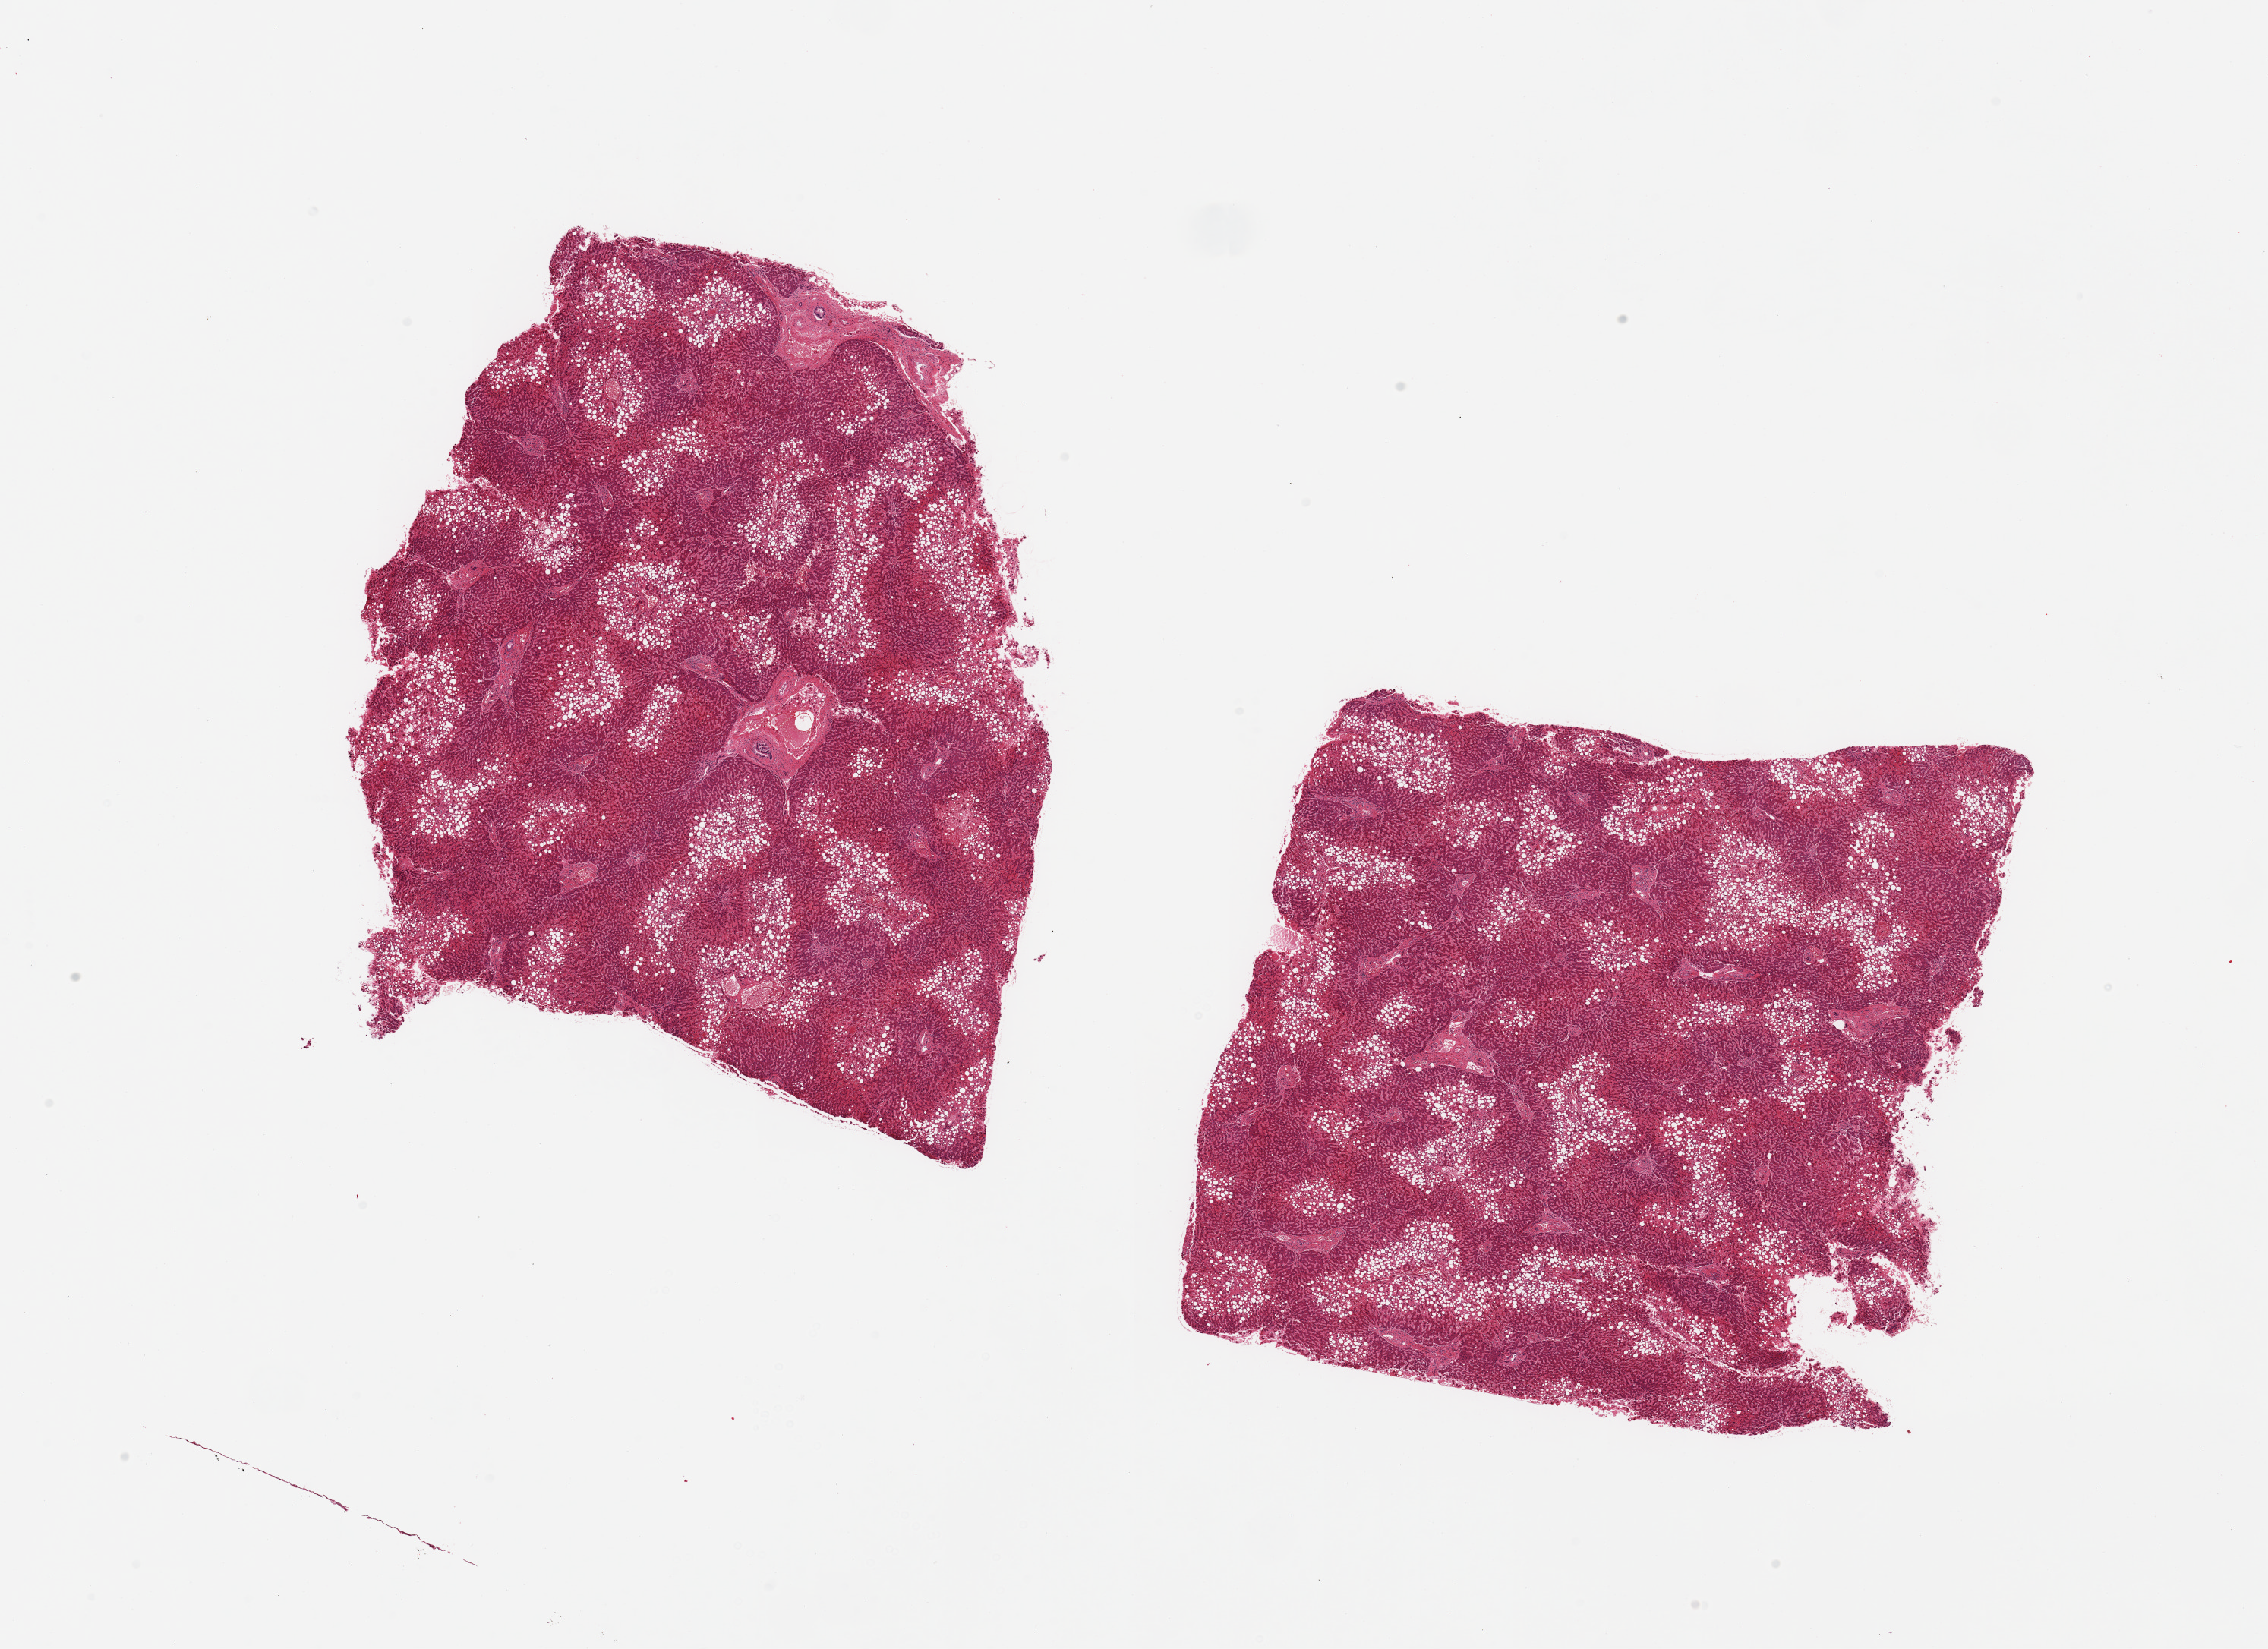
Whole-slide image, H&E stain — whole scanned area (about 23.6 x 17.2 mm) shown as a low-resolution overview, PAXgene-fixed, paraffin-embedded tissue, sampled site (target tissue): liver, donor tissue sample. Donor: male.
• reviewer comment on this tissue sample: 2 pieces, marked mascrovesicular steatosis in ~50% parenchyma, centrilobular distribution; moderate passive congestion